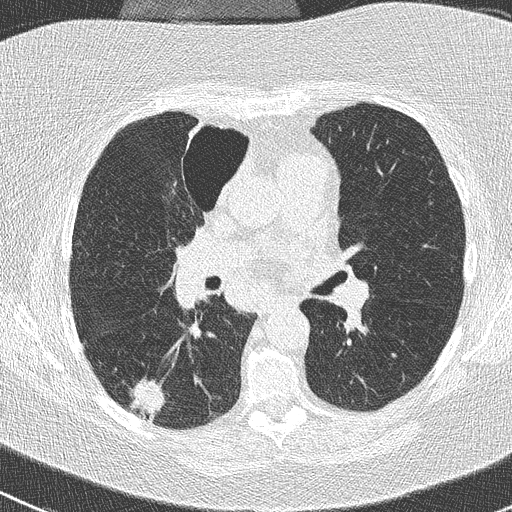
Low-dose screening chest CT, one axial slice. Slice 145 of 261 in the series (ordered by position). Lung window (W 1500 / L -600 HU). 2 mm slice thickness. 512 × 512 image matrix, field of view 310 × 310 mm.
Structures marked on this image (outlined manually by an expert reader):
- lesion 1 (tumor, lower lobe of right lung): box from (x=130, y=379) to (x=165, y=421) px